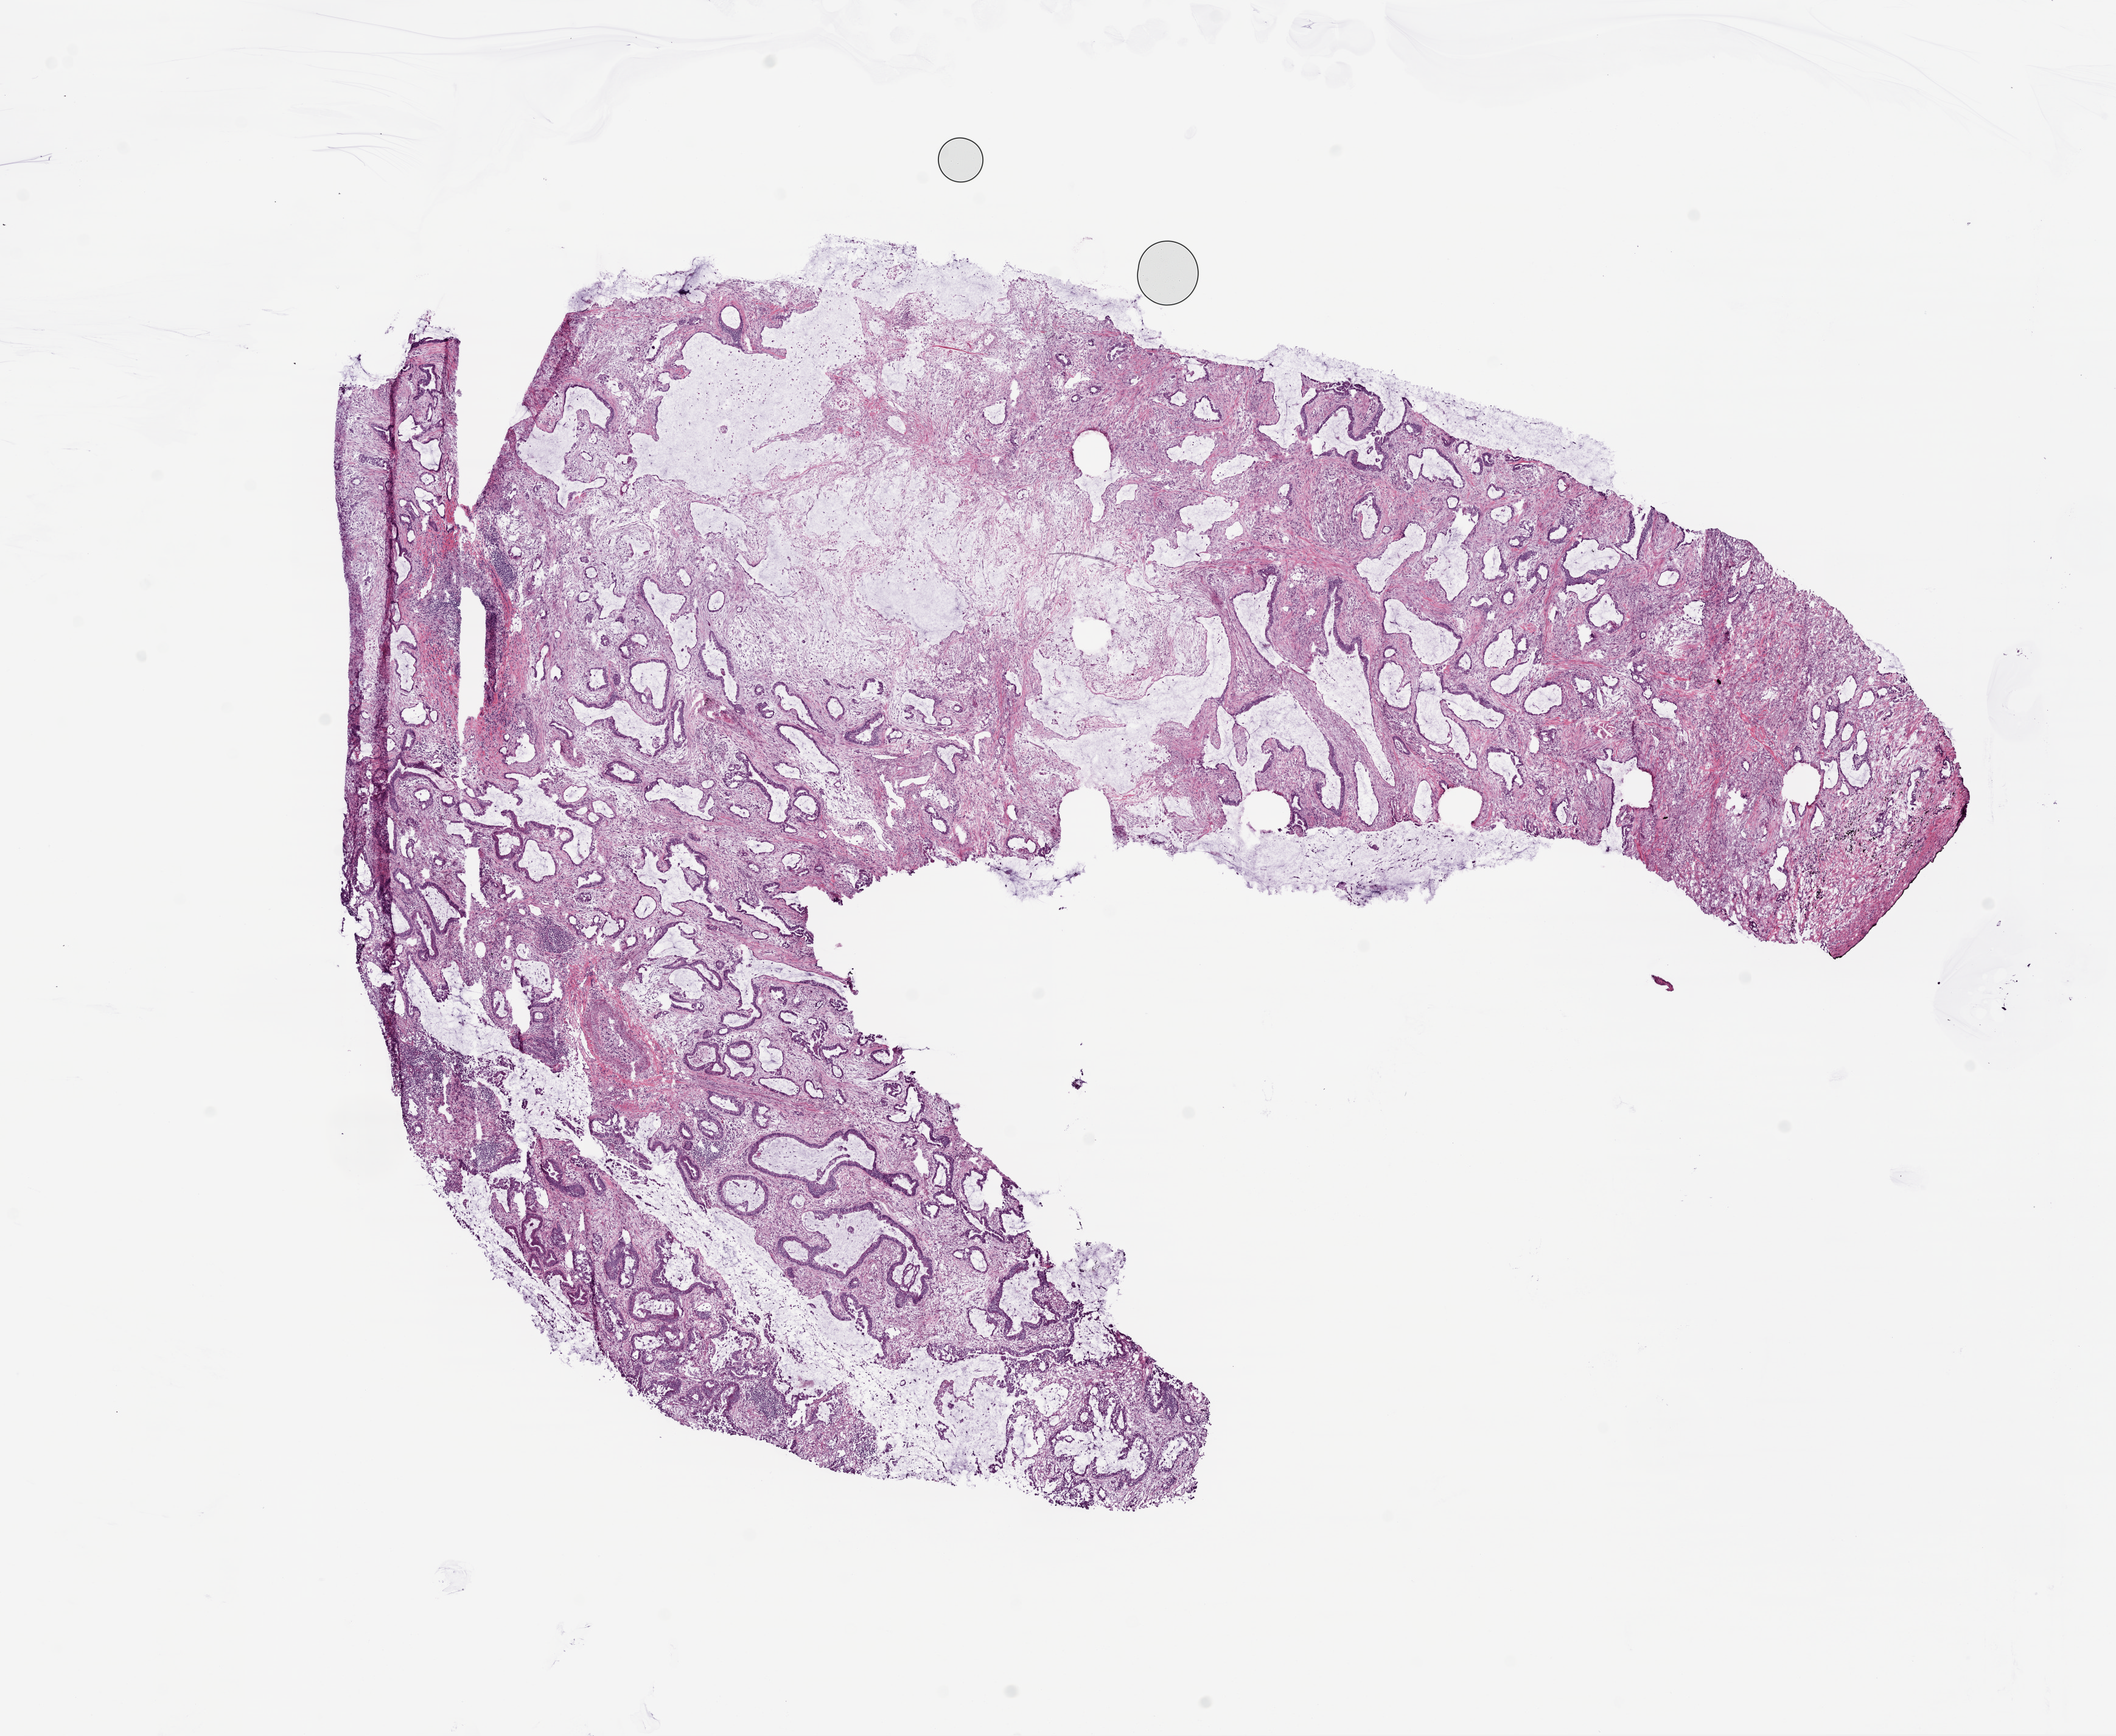
Digitized Hematoxylin and eosin (H&E) stained tissue section (whole slide) — low-resolution overview of the scanned area, about 14.0 x 11.5 mm (acquisition: 20x scan); frozen section from the top of the tissue portion; primary tumour sample from the lung. Patient: male, age at initial diagnosis 81 years. Pathologist review of this section (percent, as recorded): tumour cells 40%, tumour nuclei 60%, normal cells 0%, stromal cells 60%, necrosis 0%.
AJCC pathologic stage: IIB (6th edition). Histologic diagnosis: Mucinous adenocarcinoma. TNM: T2 N1 M0.